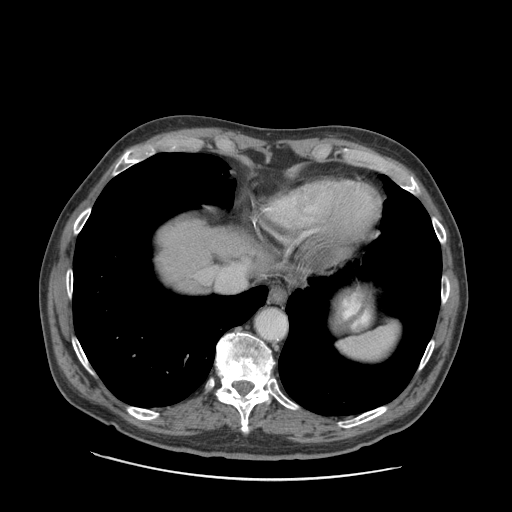
Contrast-enhanced abdominal CT (liver protocol), one axial slice. Position 79 of 89 along the scan axis. 140 kVp. Soft-tissue window (W 400 / L 40 HU). 2.5 mm slice thickness. 512 × 512 image matrix, field of view 420 × 420 mm. Case-level facts recorded for this patient, not image findings: diagnosis: hepatocellular carcinoma (patient treated with transarterial chemoembolisation; whether this scan precedes or follows treatment is not stated here); TNM stage (as recorded): Stage-I; Child-Pugh class: A; tumour nodularity: uninodular.
Structures marked on this image (semi-automatic segmentation, software-assisted and operator-edited):
- abdominal aorta: box from (x=257, y=310) to (x=286, y=339) px
- liver parenchyma outside the tumour (the mass and vessels are separate outlines, so this box may not span the whole liver): (x=157, y=218)–(x=256, y=292)